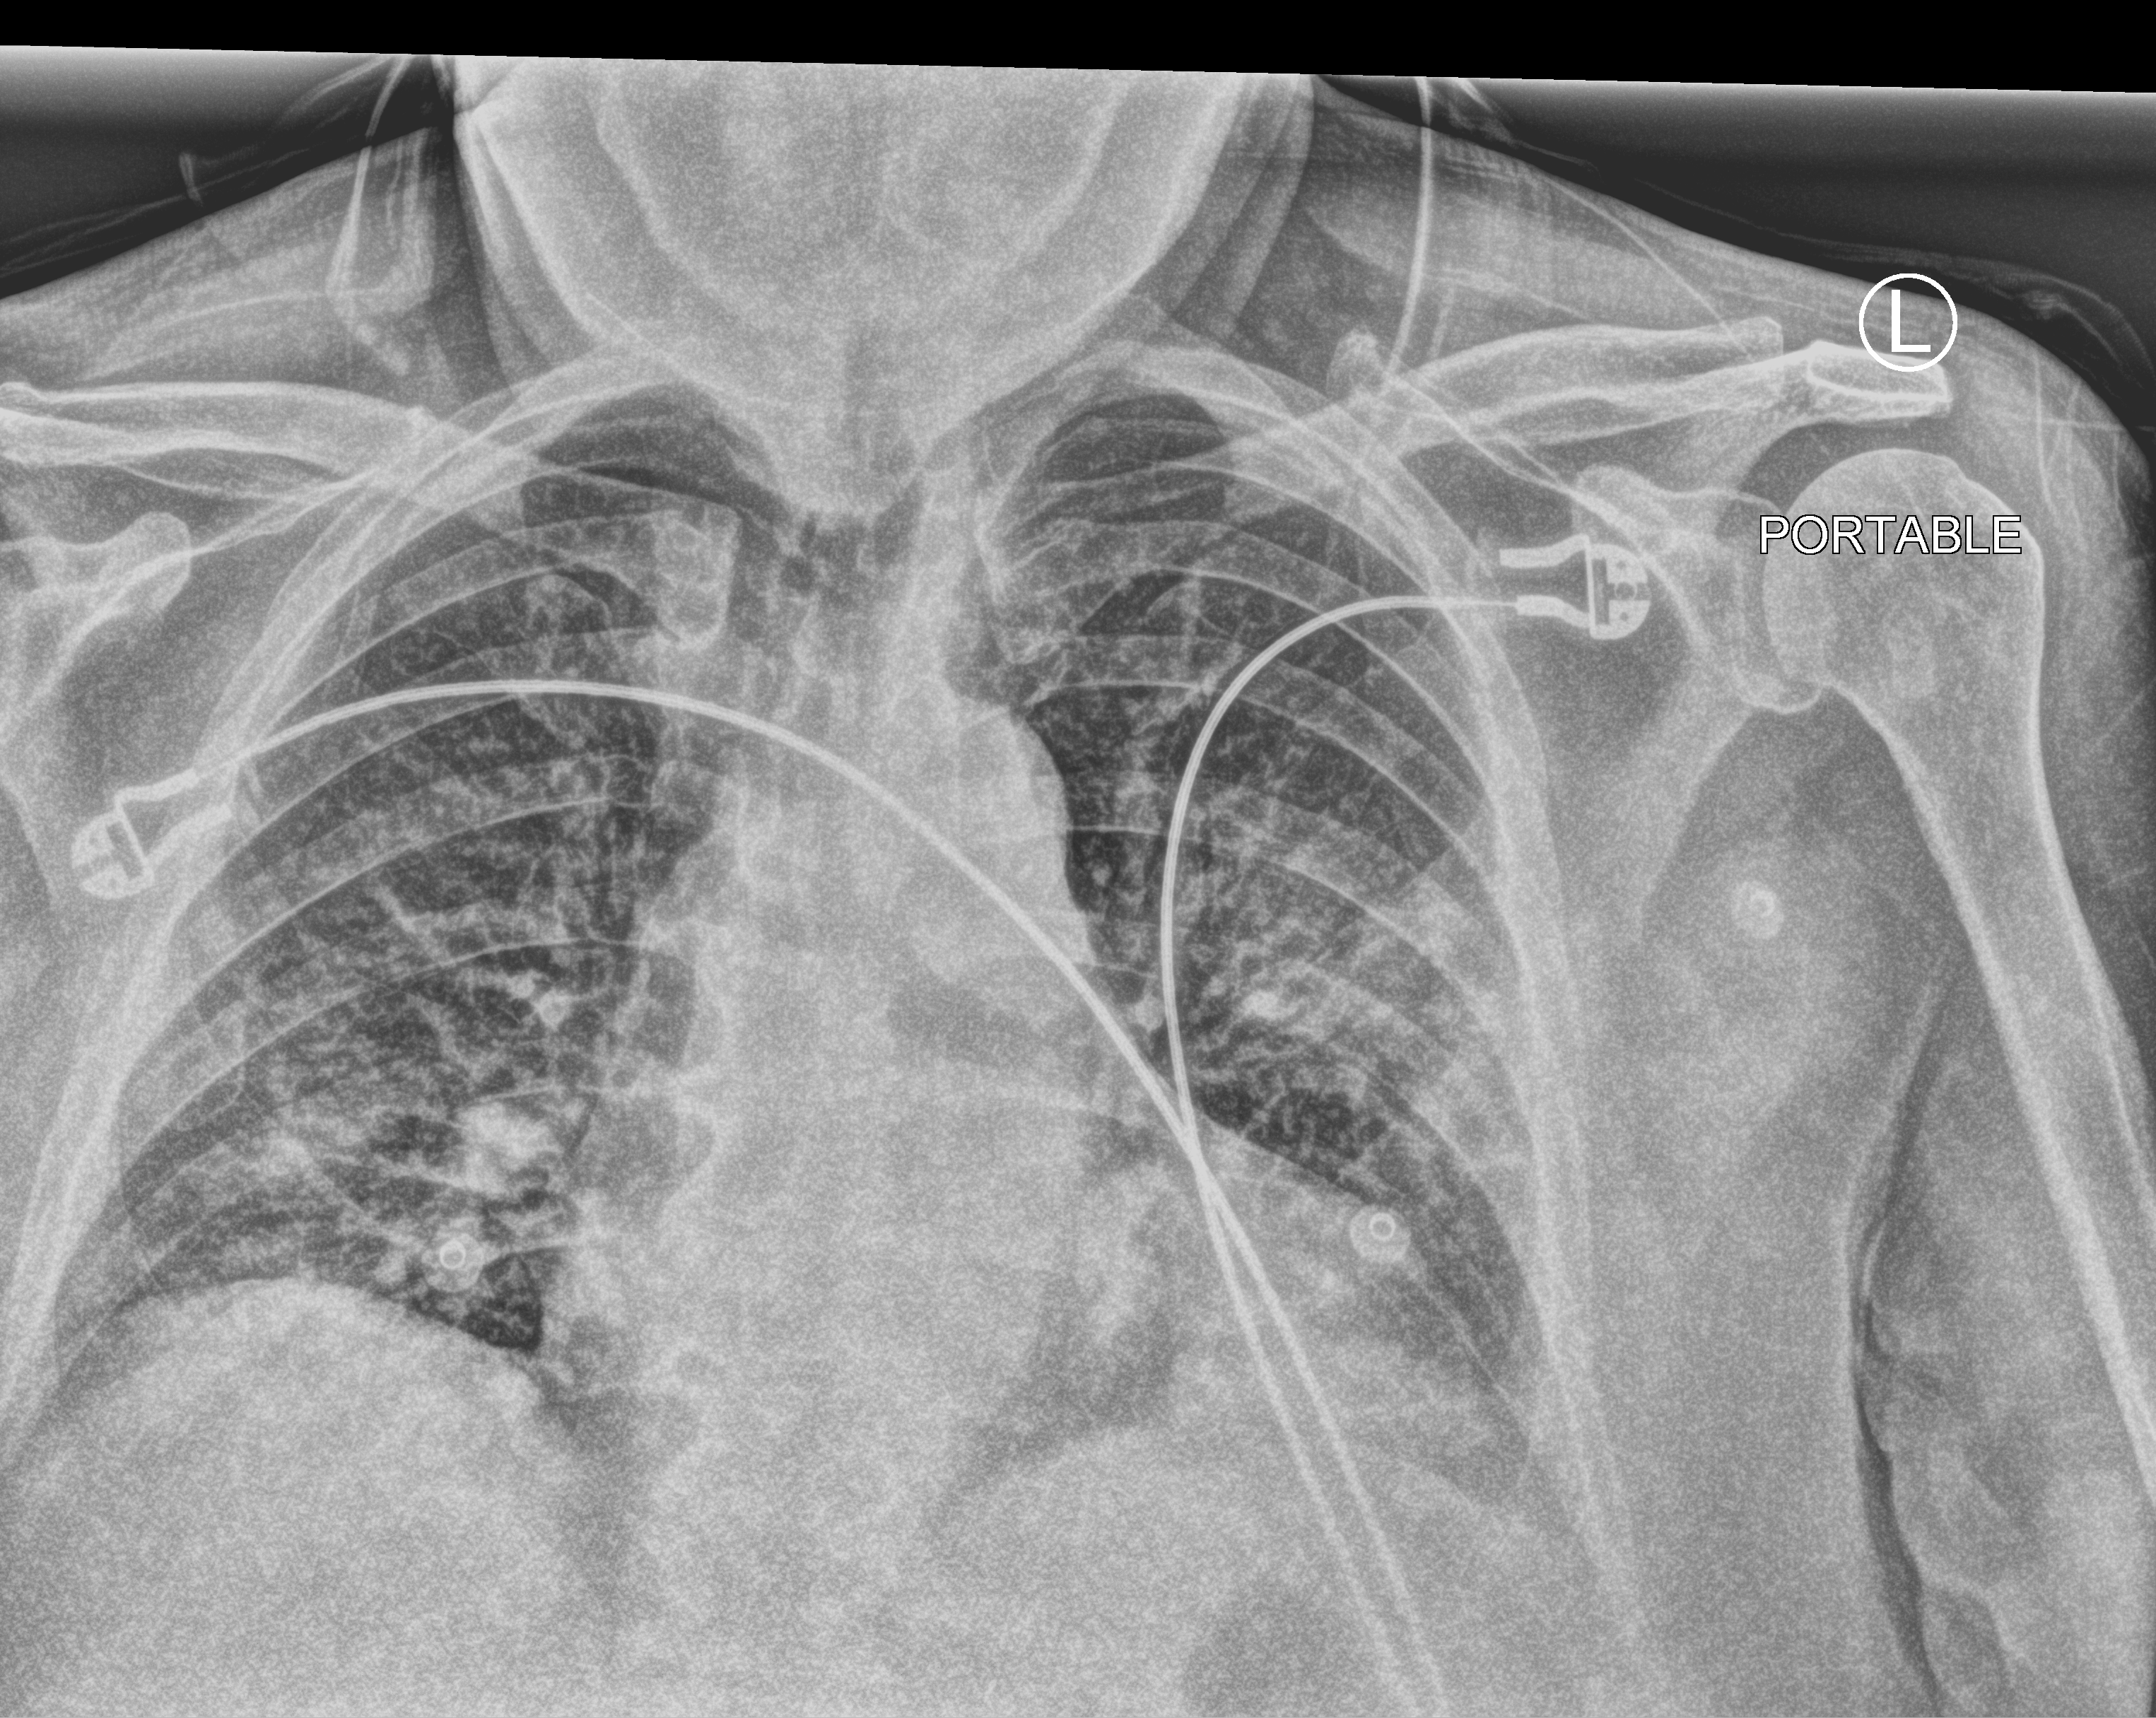
Bedside chest radiograph (computed radiography), anteroposterior (AP) projection. Patient hospitalised with COVID-19; male, aged 60–74 years.
Hospital-stay facts (about this admission, not read from this image; timing relative to this image not recorded): chronic kidney disease (admission record): no; mechanically ventilated during this hospital stay: yes; length of hospital stay: 26 days.